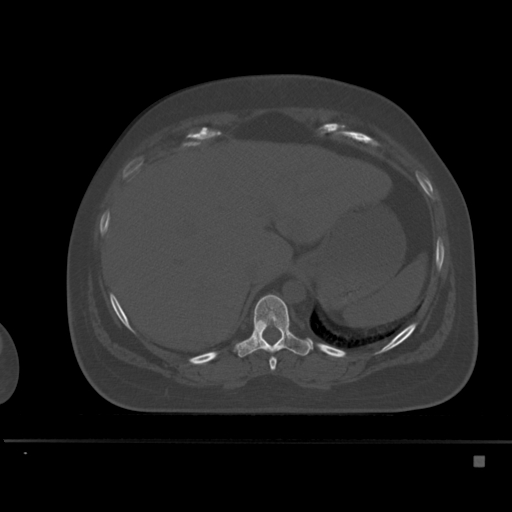
CT including the spine, one axial slice; slice 250 of 495 in the series (ordered by position); bone window (W 1800 / L 400 HU); 1.5 mm slice thickness; 512 × 512 image matrix, field of view 404 × 404 mm. Female patient, age 33 years. From the clinical record (not read from this slice): primary cancer: breast.
Structures marked on this image (semi-automatic segmentation, software-assisted and operator-edited):
- T10 vertebra: bounding box (x1, y1, x2, y2) in pixels: (235, 294, 312, 358)
- T9 vertebra: (269, 356, 277, 371)